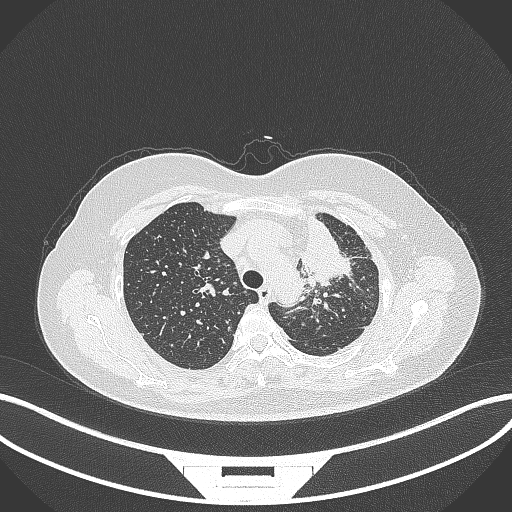
Chest CT, one axial slice. Position 256 of 348 along the scan axis. Reconstruction kernel B70f. Lung window (W 1500 / L -600 HU). 512 × 512 image matrix, field of view 400 × 400 mm. Patient: female, 49 years. From the clinical record (not read from this slice): clinical TNM (as recorded): T1c N0 M1.
Outlined on this slice (bounding box drawn by a radiologist):
- lung tumour (recorded histology: adenocarcinoma): bounding box <296,209,355,289> (left, top, right, bottom; pixels)